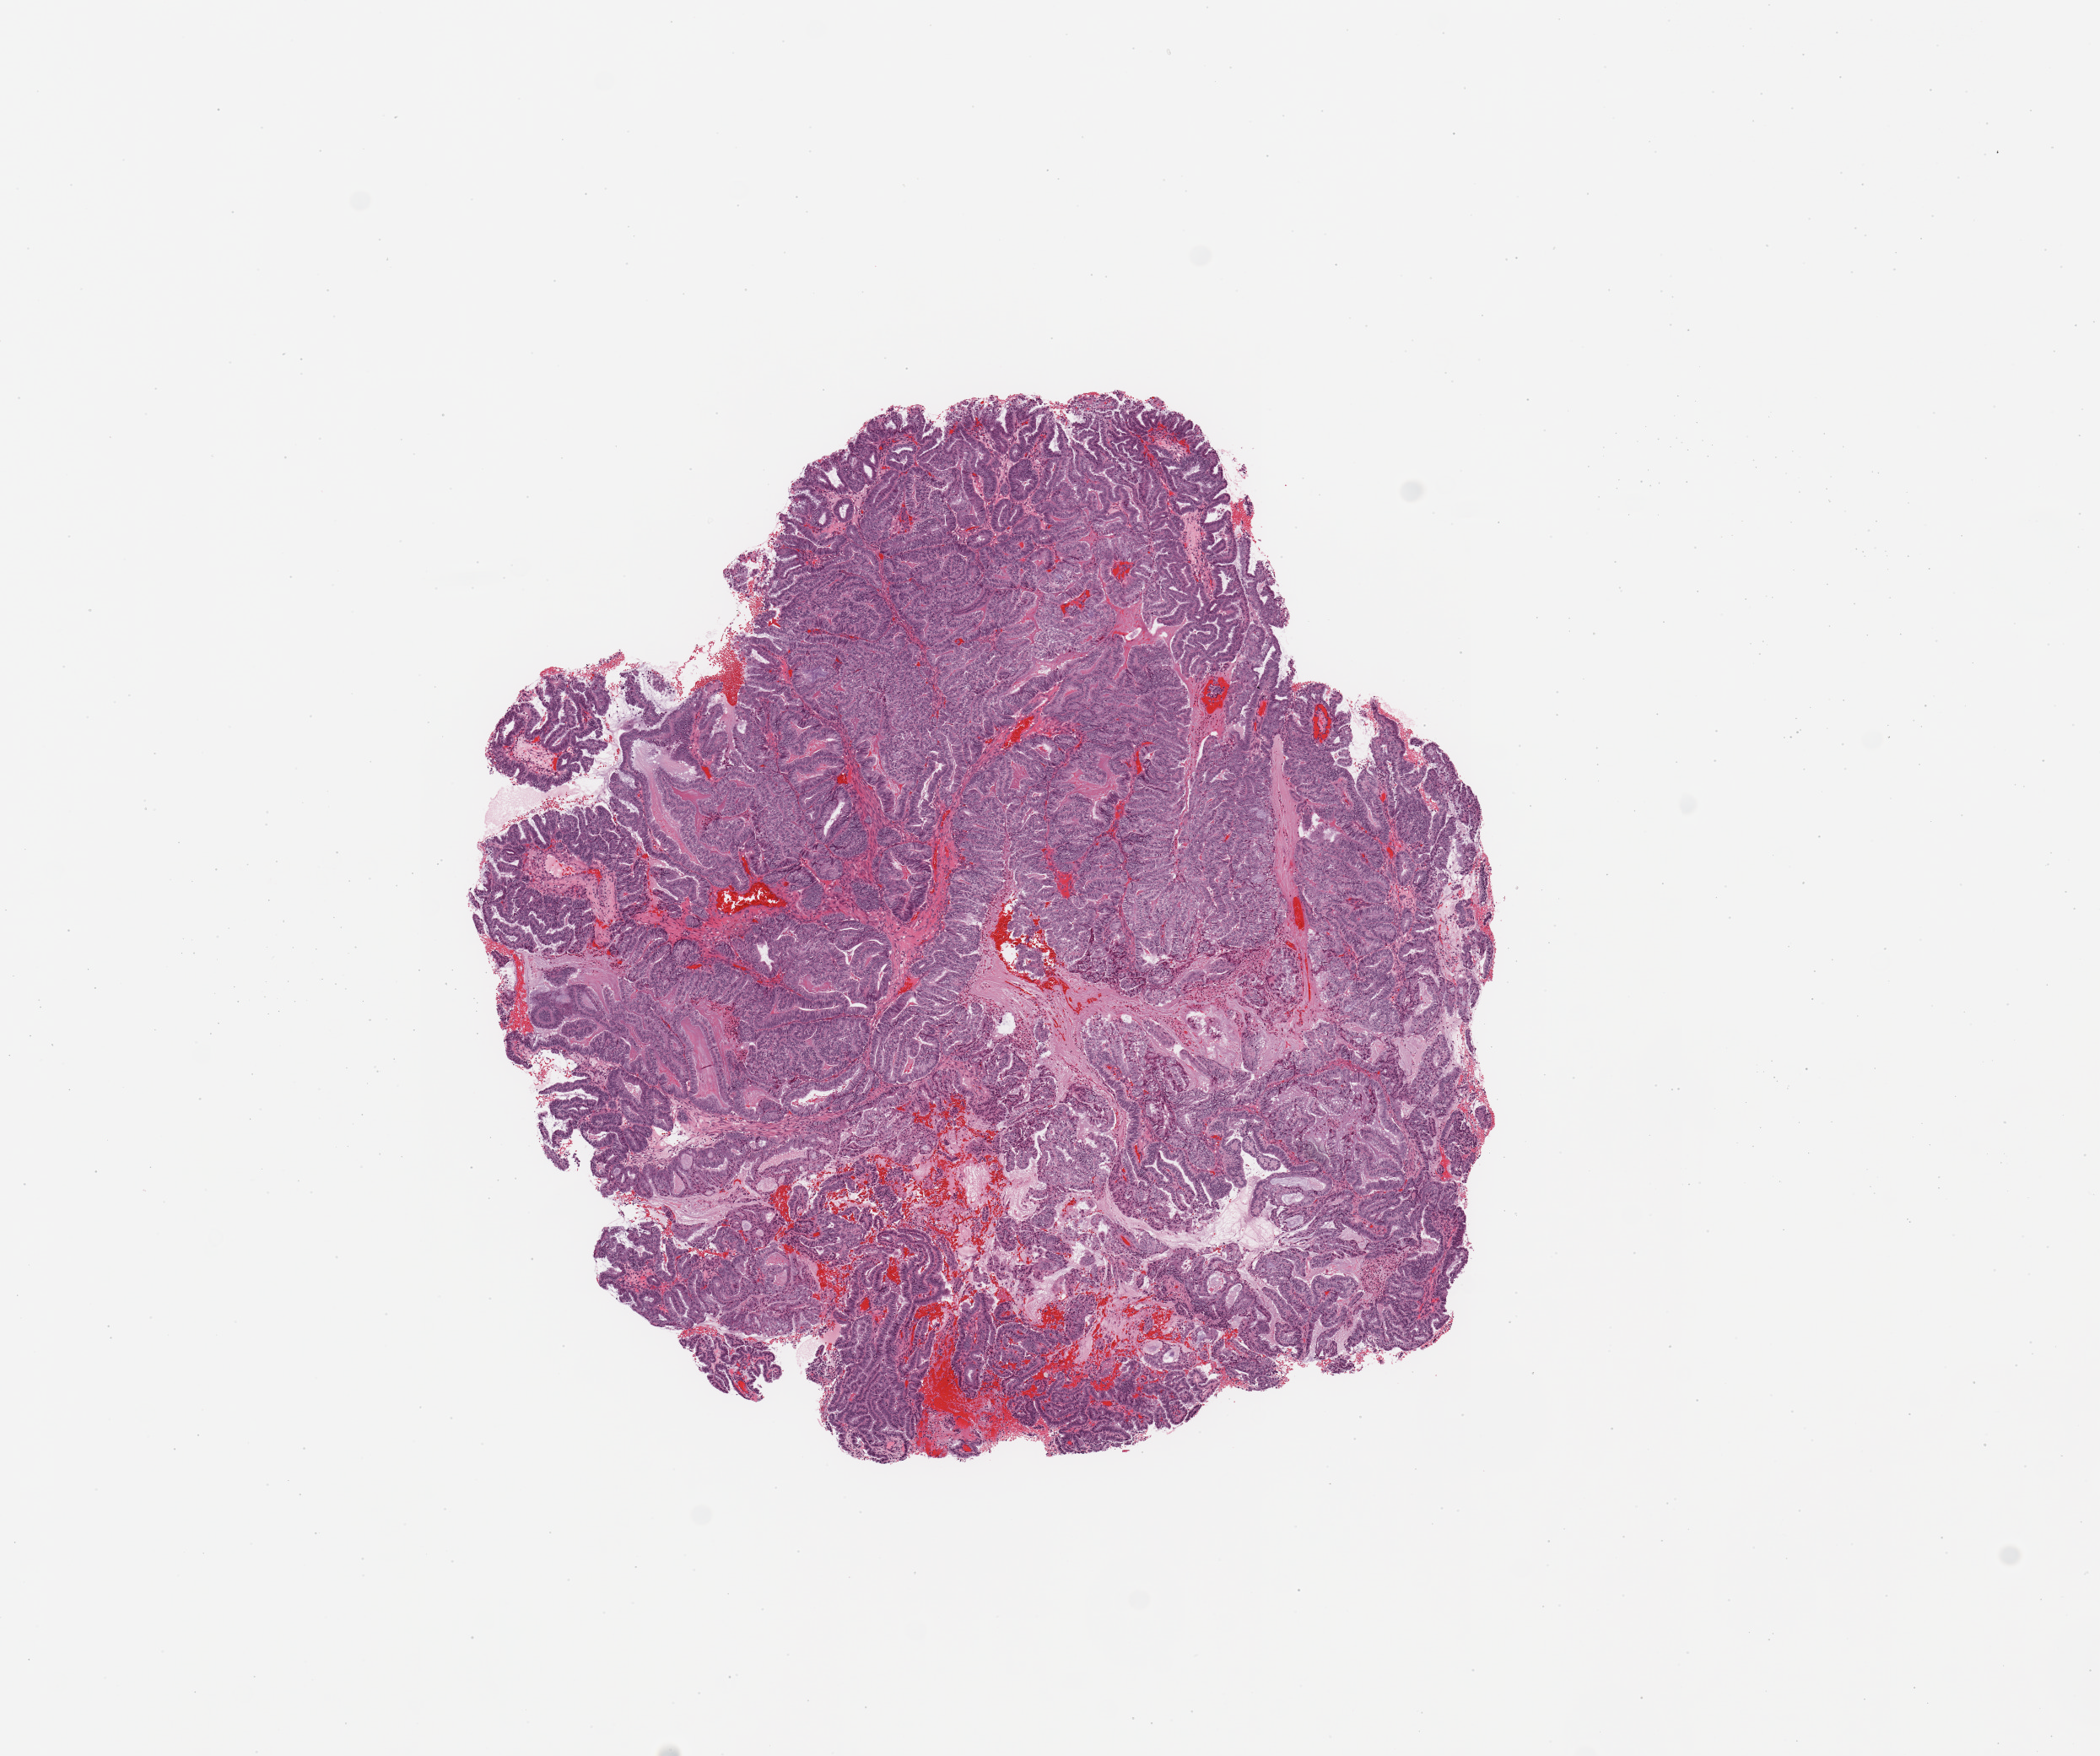
Whole-slide histology image, H&E-stained — low-resolution overview of the scanned area, about 9.8 x 8.2 mm (acquisition: 20x scan); tumour tissue sample, sampled site: uterus. 80-year-old female patient.
Histologic diagnosis: Endometrioid adenocarcinoma, NOS.